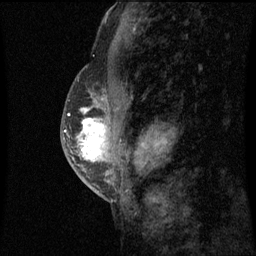
Breast MRI (dynamic contrast-enhanced), one sagittal slice. Position 30 of 60 along the scan axis. Dynamic contrast-enhanced series, image 2 of 3 at this slice position (ordered by acquisition). 1.5 T. TE 4.2 ms, TR 8.9 ms. 2 mm slice thickness. 256 × 256 image matrix. Female patient, age 50 years. Case-level facts recorded for this patient, not image findings: setting: breast cancer imaged before/during neoadjuvant chemotherapy; receptor status: triple-negative.
Annotated regions visible in this slice (semi-automatically segmented with operator editing):
- analysis volume of interest (the breast-tissue region the enhancement analysis was run in; not a lesion): bounding box <68,80,109,169> (left, top, right, bottom; pixels)
- tumour enhancement mask (voxels above the 70 % enhancement threshold inside the analysis volume of interest): <82,110,106,161>